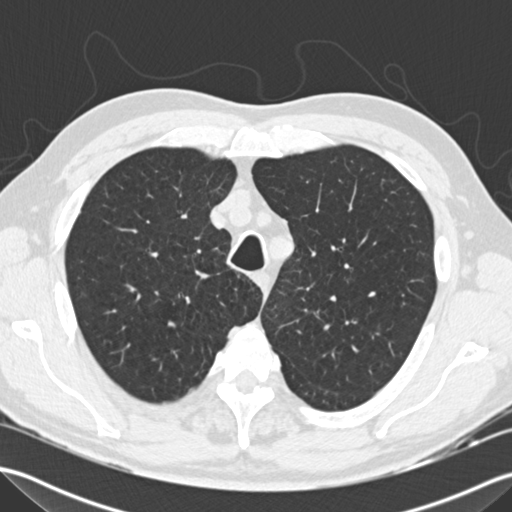
Chest CT (low-dose screening protocol), one axial image. First (baseline) screen. Lung window (W 1500 / L -600 HU). Male participant, aged 66 years at enrolment. Current smoker at enrolment.
- Expert reader's lesion annotation, bounding box (x1, y1, x2, y2) in pixels: (289, 298, 337, 340).
- Screening reader's record for this exam: no non-calcified nodule ≥4 mm recorded.
- Official screen result: negative screen, minor abnormalities not suspicious for lung cancer.
- Participant outcome: lung cancer diagnosed 679 days after this screen — squamous cell carcinoma, NOS, left upper lobe, poorly differentiated (G3), stage IA (AJCC 6th edition), 15 mm at pathology.